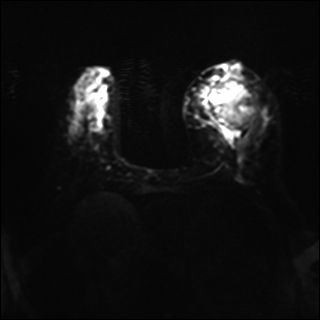
Breast MRI, one axial slice. Position 13 of 37 along the scan axis. Diffusion-weighted series; image 2 of 4 stored at this slice position (different b-values; order by instance number). 1.5 T. 320 × 320 image matrix, field of view 320 × 320 mm. Female patient.
Structures marked on this image (manually delineated by an expert):
- tumour on diffusion-weighted imaging: bounding box (x1, y1, x2, y2) in pixels: (209, 81, 259, 129)